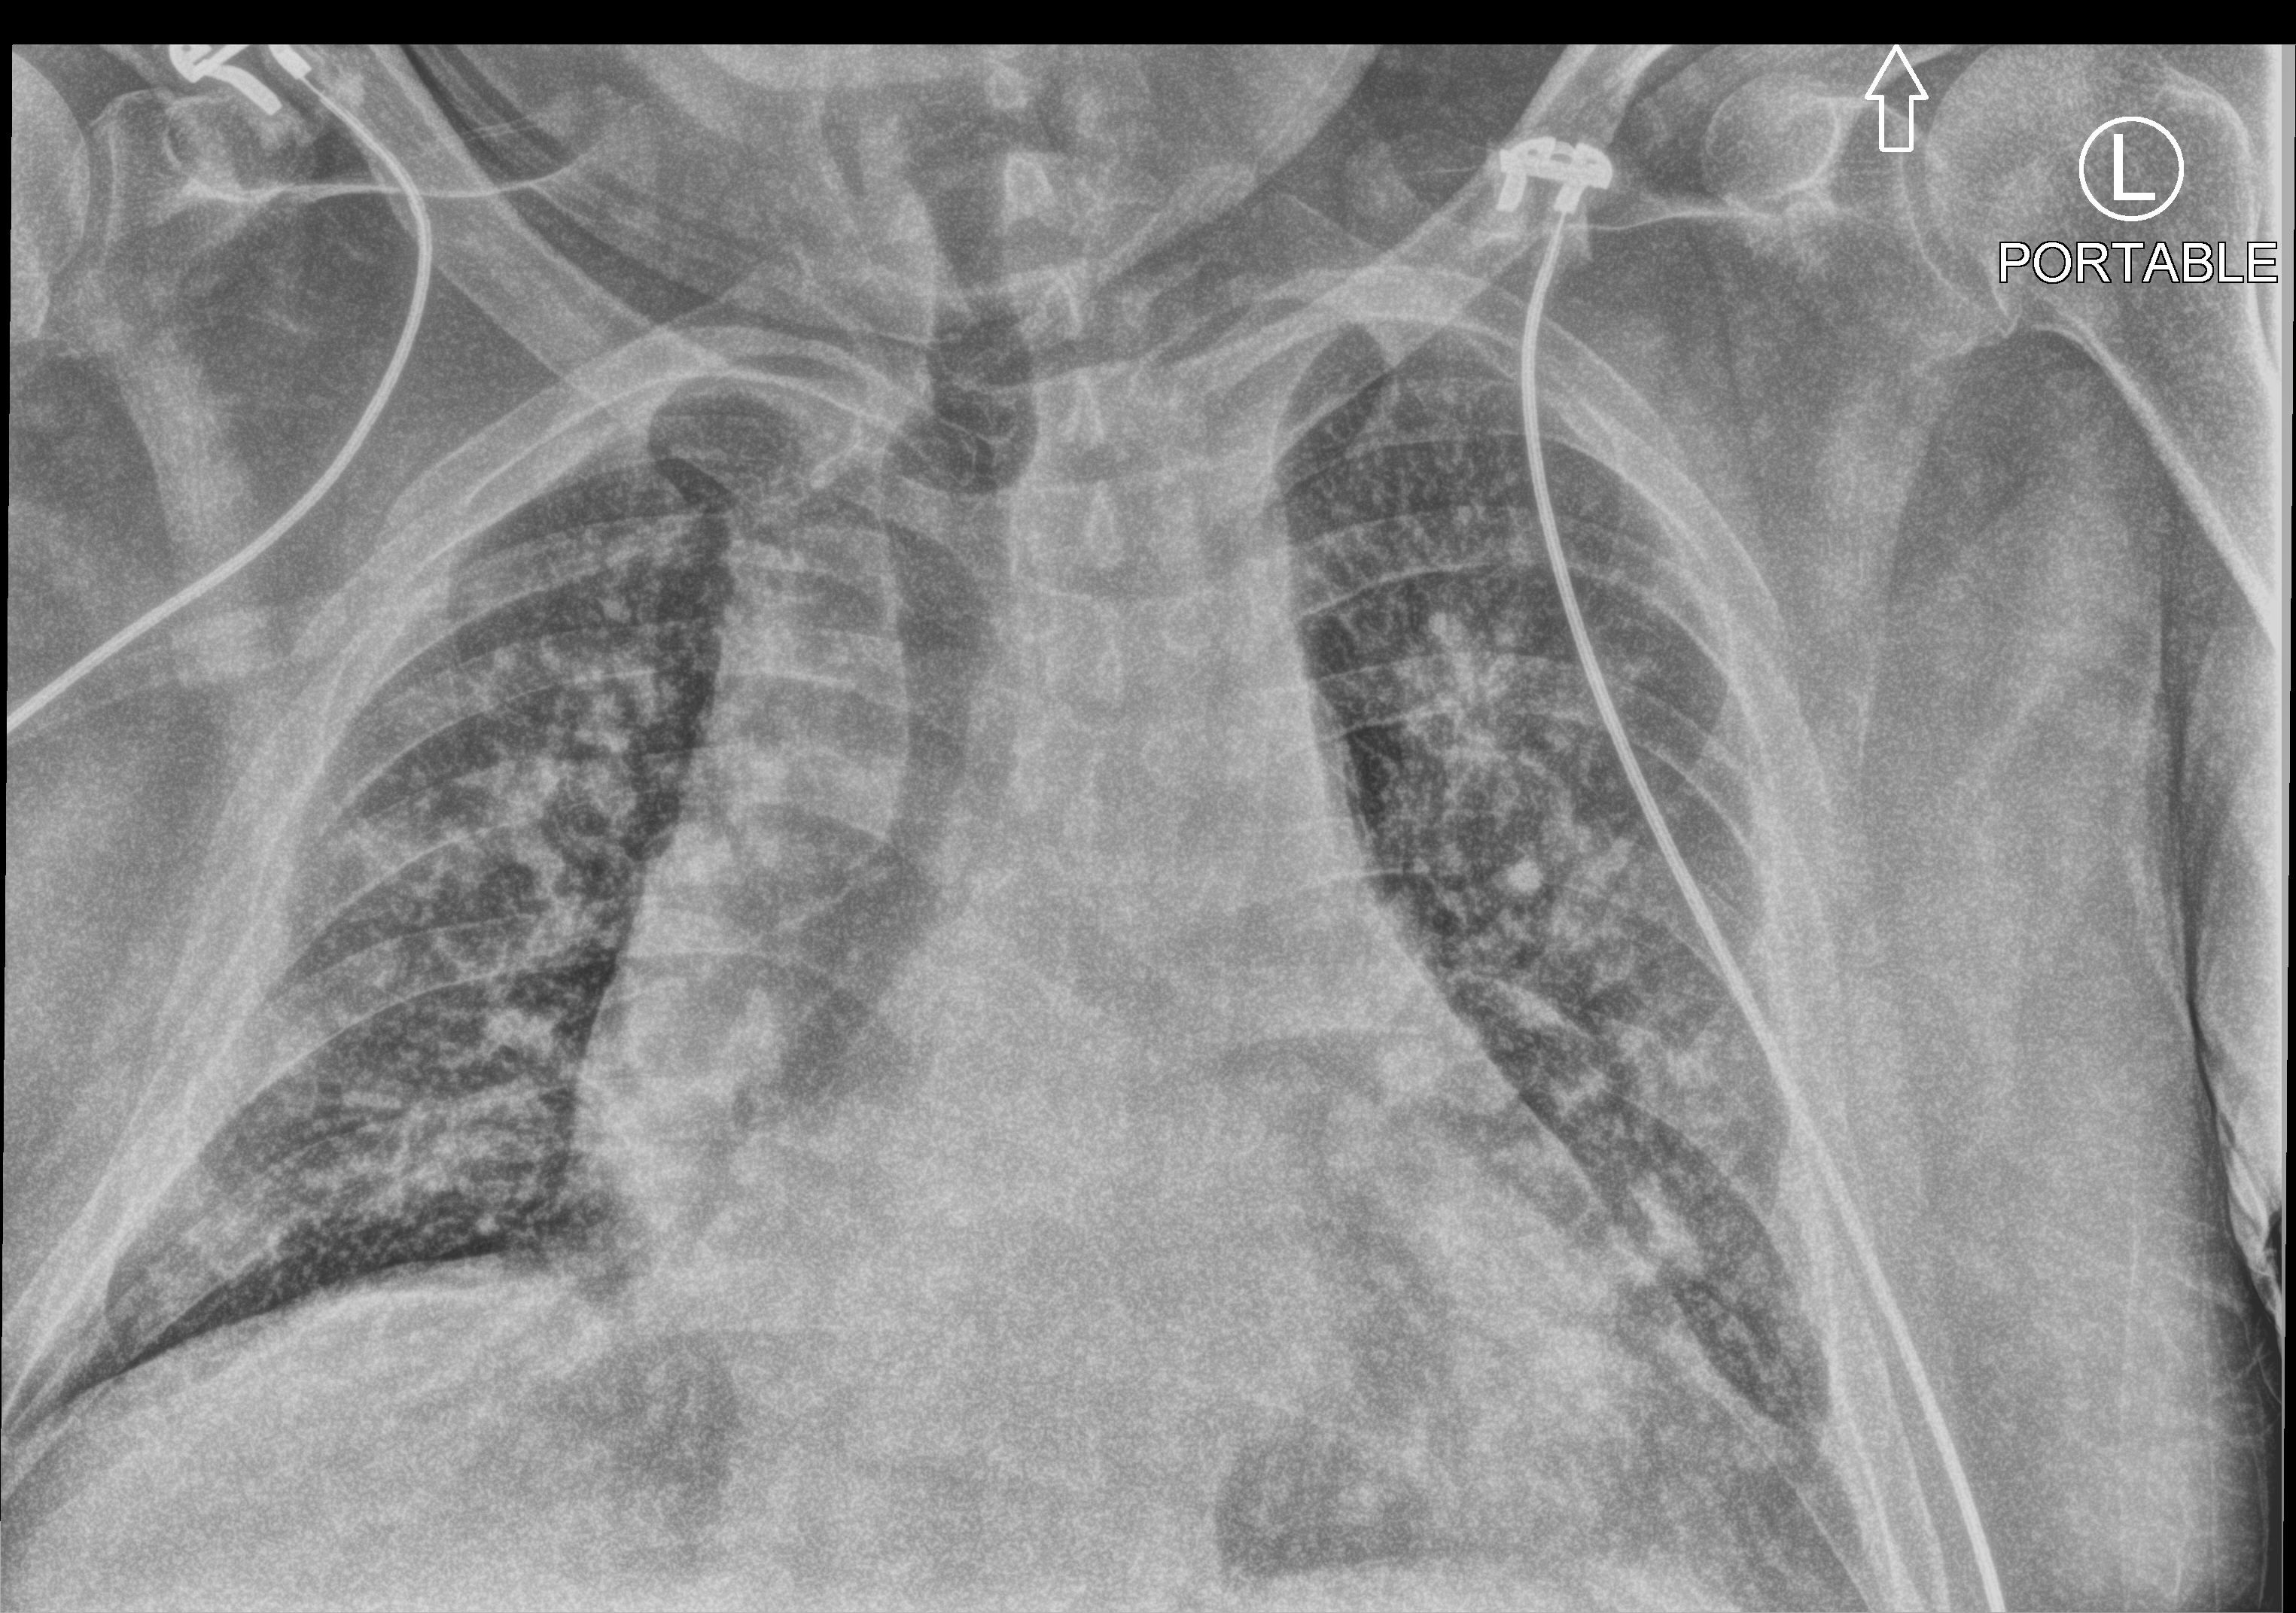
Portable chest radiograph; anteroposterior (AP) projection. Male patient hospitalised with COVID-19, age 18–59 years.
Hospital-stay facts (about this admission, not read from this image; timing relative to this image not recorded):
- chronic kidney disease (admission record): yes
- smoking status (admission record): former
- COPD (admission record): no